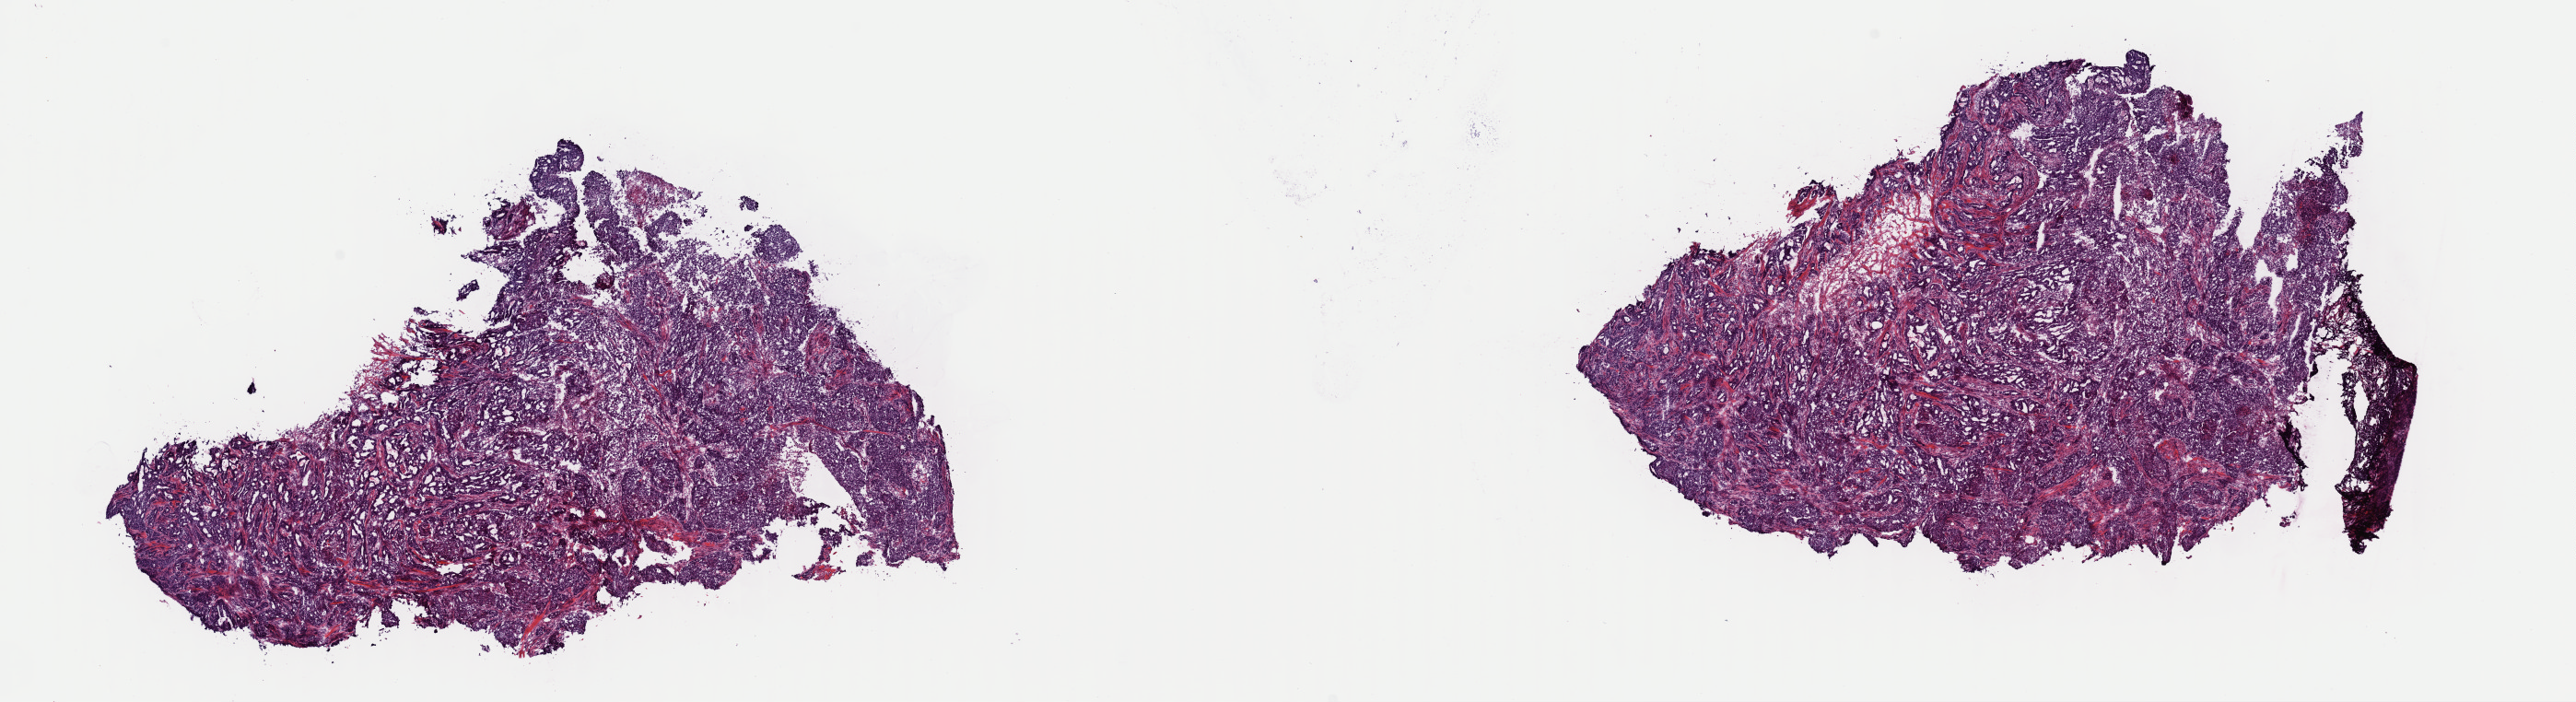
Whole-slide histology image, H&E-stained — whole scanned area (about 22.1 x 6.0 mm) shown as a low-resolution overview. Frozen section from the top of the tissue portion. Primary tumour sample from the breast. Patient: female, age at initial diagnosis 48 years. Slide review estimates, as recorded: tumour cells 60%, tumour nuclei 85%, normal cells 0%, stromal cells 22%, necrosis 18%. Inflammatory infiltration, as recorded: lymphocyte infiltration 5%, monocyte infiltration 2%, neutrophil infiltration 2%.
AJCC pathologic stage: IIA (7th edition). TNM: T2 N0 M0. Histologic diagnosis: Infiltrating duct carcinoma, NOS. Lymph nodes positive (case pathology): 0 of 2 examined.